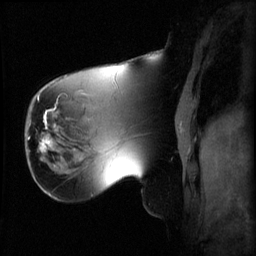
Breast MRI (dynamic contrast-enhanced), one sagittal slice. 3 images stored at this slice position (order not interpretable as contrast timing). 1.5 T. TE 4.2 ms, TR 8.2 ms. 2.2 mm slice thickness. 256 × 256 image matrix, field of view 220 × 220 mm. Female patient, age 62 years.
Annotated regions visible in this slice (semi-automatic segmentation, software-assisted and operator-edited):
- analysis volume of interest (the breast-tissue region the enhancement analysis was run in; not a lesion): bounding box (x1, y1, x2, y2) in pixels: (26, 126, 59, 165)
- tumour enhancement mask (voxels above the 70 % enhancement threshold inside the analysis volume of interest): (28, 126, 51, 153)